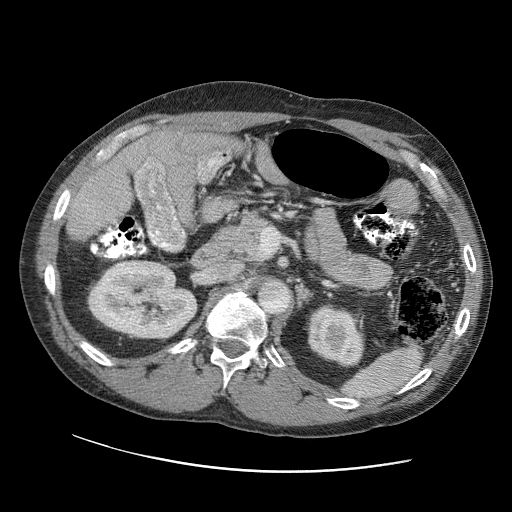
Contrast-enhanced abdominal CT (liver protocol), one axial slice. Reconstruction kernel STANDARD. Soft-tissue window (W 400 / L 40 HU). 2.5 mm slice thickness. 512 × 512 image matrix, field of view 400 × 400 mm. From the clinical record (not read from this slice): diagnosis: hepatocellular carcinoma (patient treated with transarterial chemoembolisation; whether this scan precedes or follows treatment is not stated here); TNM stage (as recorded): Stage-IIIC; Child-Pugh class: B; tumour nodularity: uninodular.
Annotated regions visible in this slice (semi-automatic segmentation, software-assisted and operator-edited):
- liver parenchyma outside the tumour (the mass and vessels are separate outlines, so this box may not span the whole liver): bounding box <110,130,224,172> (left, top, right, bottom; pixels)
- liver vessels: <121,133,216,170>